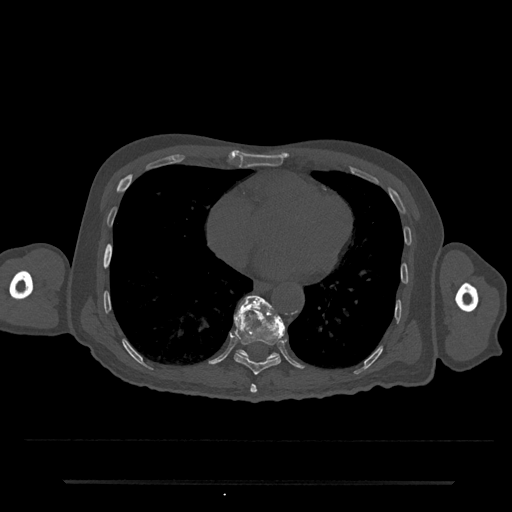
CT including the spine, one axial slice; slice 354 of 797 in the series (ordered by position); bone window (W 1800 / L 400 HU); 512 × 512 image matrix. Male patient, age 74 years. Case-level facts recorded for this patient, not image findings: primary cancer: prostate.
Outlined on this slice (semi-automatically segmented with operator editing):
- T10 vertebra: box from (x=237, y=295) to (x=285, y=360) px
- T8 vertebra: (x=250, y=384)–(x=257, y=394)
- T9 vertebra: (x=234, y=296)–(x=285, y=375)